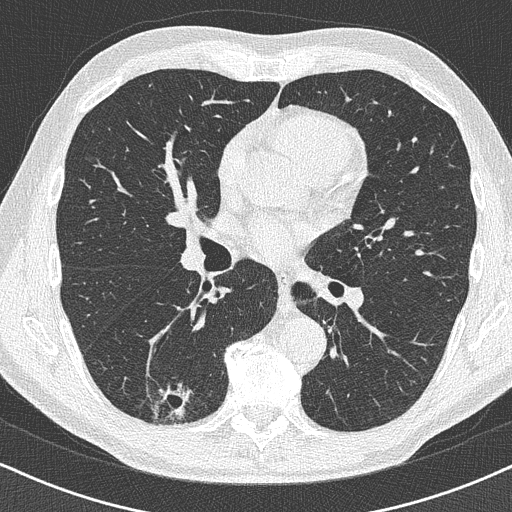
Axial slice from a low-dose chest CT screening exam. Baseline screening round. Lung window (W 1500 / L -600 HU). 1 mm slice thickness. Lung (sharp) reconstruction kernel (B50f). Slice 209 of 438 in the series. Male participant, aged 63 years at enrolment. Former smoker at enrolment.
Expert-annotated lung lesion, bounding box <137,372,208,430> (left, top, right, bottom; pixels). Screening reader's record for this exam (one nodule recorded; not confirmed to be the boxed lesion): non-calcified nodule or mass ≥4 mm, right lower lobe, 16 × 13 mm, poorly defined margins. Official screen result: positive, change unspecified: nodule(s) >= 4 mm or enlarging nodule(s), mass(es), or other non-specific abnormalities suspicious for lung cancer. Lung cancer was diagnosed 74 days after this screen: adenocarcinoma, NOS, right lower lobe, moderately differentiated (G2), stage IA (AJCC 6th edition), 20 mm at pathology.